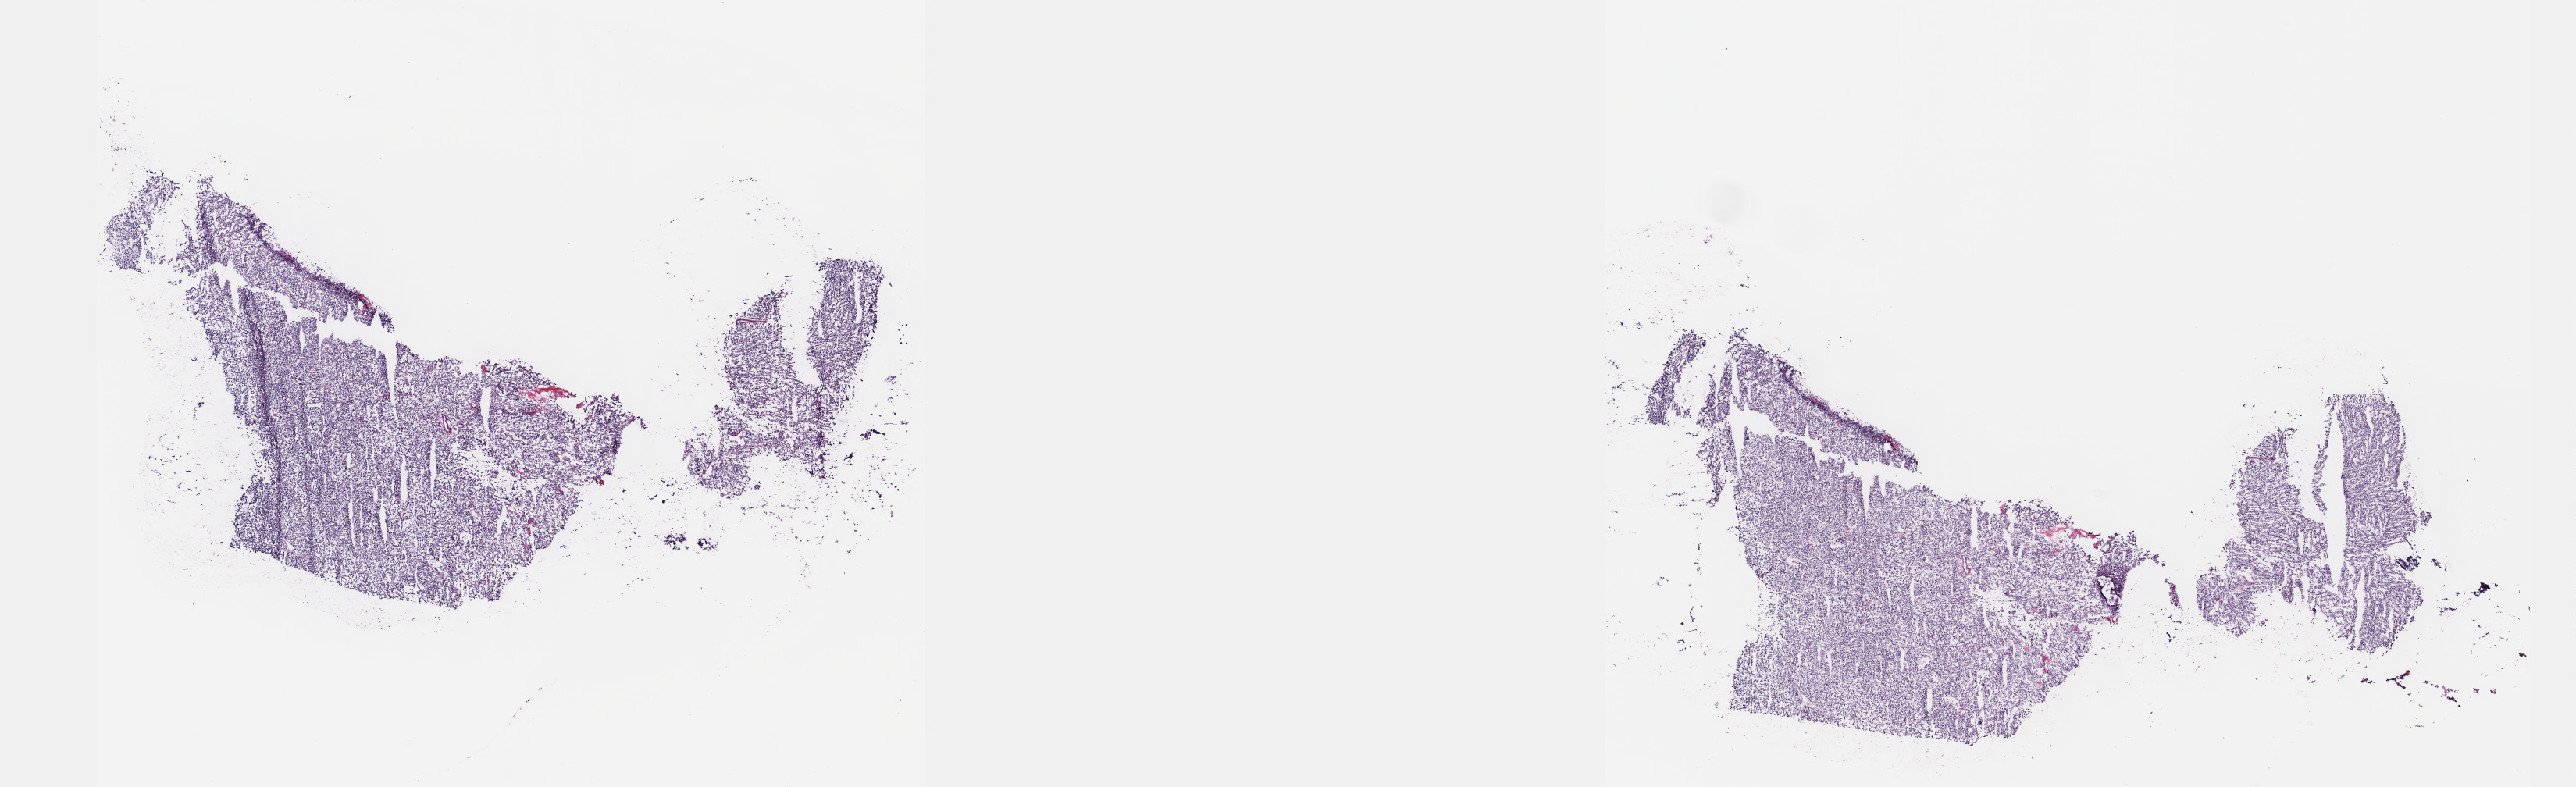
H&E whole-slide image, low-resolution overview of the scanned area, about 26.7 x 8.1 mm; frozen section; sample: primary tumour, adrenal gland. Female, age 63 years at initial diagnosis. Pathologist review of this section (percent, as recorded): tumour cells 100%, tumour nuclei 80%, normal cells 0%, stromal cells 0%, necrosis 0%. Inflammatory infiltration, as recorded: lymphocyte infiltration 1%, monocyte infiltration 0%, neutrophil infiltration 0%.
- laterality: left
- pathologic diagnosis: Pheochromocytoma, malignant